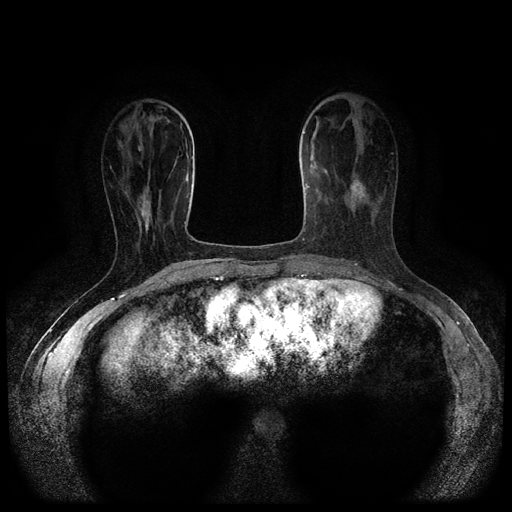
Breast MRI (dynamic contrast-enhanced, multi-phase), one axial slice. Slice 32 of 116 in the series (ordered by position). Dynamic contrast-enhanced series, time point 2 of 5 at this slice position (early post-contrast). 1.5 T. TE 2.6 ms, TR 5.4 ms. 512 × 512 image matrix, field of view 340 × 340 mm. Female patient, age 47 years.
Outlined on this slice (semi-automatic segmentation, software-assisted and operator-edited):
- breast lesion (labelled 'tumour' in the annotation; benign lesions carry a separate 'benign' label): bounding box <347,177,366,210> (left, top, right, bottom; pixels)
- breast lesion (labelled 'tumour' in the annotation; benign lesions carry a separate 'benign' label): <137,188,152,232>